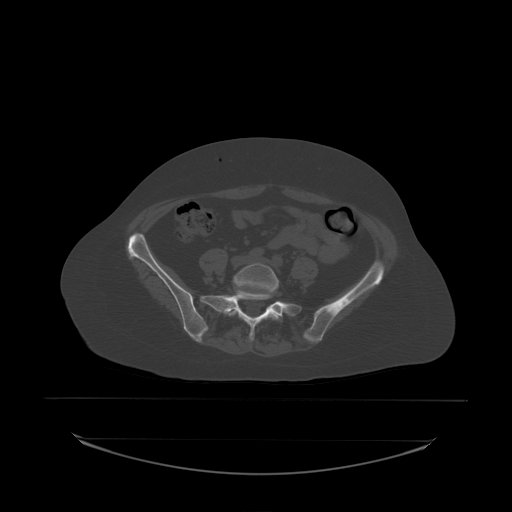
CT including the spine, one axial slice; position 34 of 242 along the scan axis; bone window (W 1800 / L 400 HU); 2.5 mm slice thickness; 512 × 512 image matrix, field of view 500 × 500 mm. Patient: female, 53 years. Case-level facts recorded for this patient, not image findings: primary cancer: lung; vertebrae with lytic lesions (as recorded): T7, L1.
Annotated regions visible in this slice (semi-automatically segmented with operator editing):
- L5 vertebra: box from (x=229, y=263) to (x=280, y=320) px